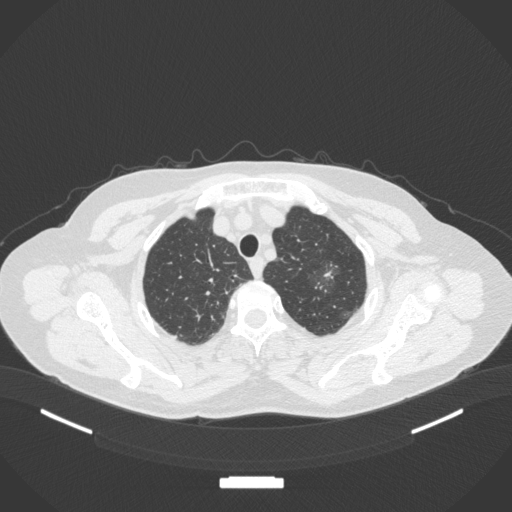
Chest CT, one axial slice; position 307 of 369 along the scan axis; reconstruction kernel B31f; 120 kVp; lung window (W 1500 / L -600 HU); 512 × 512 image matrix. Patient: female, 64 years. From the clinical record (not read from this slice): clinical TNM (as recorded): T1c N0 M0.
Structures marked on this image (bounding box drawn by a radiologist):
- lung tumour (recorded histology: adenocarcinoma): bounding box (x1, y1, x2, y2) in pixels: (310, 255, 344, 295)